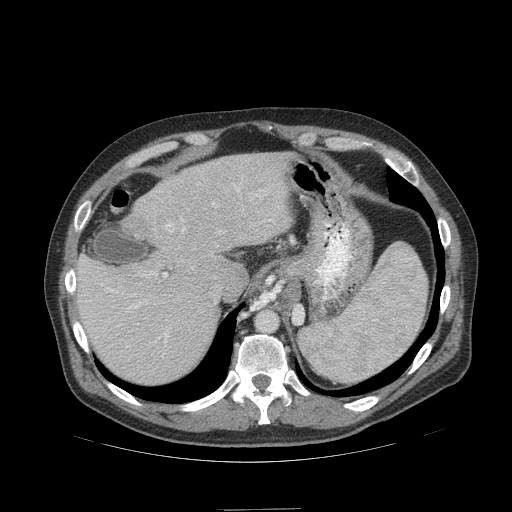
Contrast-enhanced abdominal CT (liver protocol), one axial slice. Position 78 of 99 along the scan axis. Reconstruction kernel STANDARD. 140 kVp. Soft-tissue window (W 400 / L 40 HU). 2.5 mm slice thickness. 512 × 512 image matrix, field of view 440 × 440 mm. Case-level facts recorded for this patient, not image findings: diagnosis: hepatocellular carcinoma (patient treated with transarterial chemoembolisation; whether this scan precedes or follows treatment is not stated here); TNM stage (as recorded): Stage-I.
Annotated regions visible in this slice (semi-automatically segmented with operator editing):
- liver parenchyma outside the tumour (the mass and vessels are separate outlines, so this box may not span the whole liver): bounding box [x1, y1, x2, y2] px = [76, 152, 292, 384]
- liver vessels: [100, 176, 279, 347]